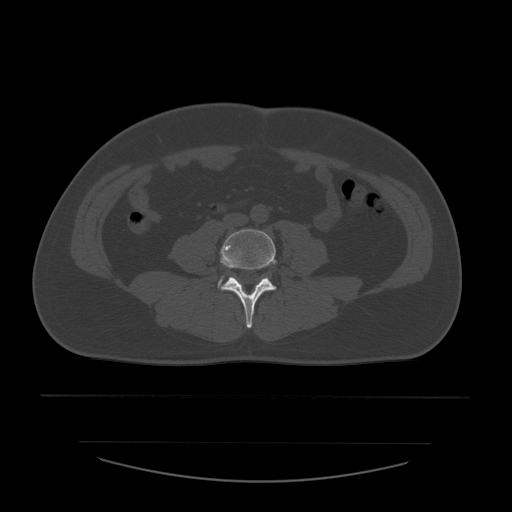
CT including the spine, one axial slice. Slice 141 of 532 in the series (ordered by position). Reconstruction kernel STANDARD. Bone window (W 1800 / L 400 HU). 512 × 512 image matrix, field of view 441 × 441 mm. Patient age 44 years. From the clinical record (not read from this slice): primary cancer: soft tissue sarcoma.
Structures marked on this image (semi-automatically segmented with operator editing):
- L4 vertebra: box from (x=221, y=229) to (x=276, y=328) px
- L5 vertebra: (x=219, y=279)–(x=222, y=287)